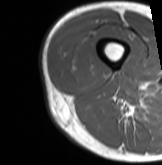
MRI of an extremity soft-tissue mass, one axial slice; position 13 of 61 along the scan axis; MR volume resampled by the dataset authors to the PET/CT grid (not the native acquisition matrix); 3.27 mm slice thickness; 162 × 165 image matrix. Male patient. Case-level facts recorded for this patient, not image findings: histological type: poorly differentiated synovial sarcoma; grade: high; site of the primary tumour: right buttock.
Structures marked on this image (expert contour drawn on MRI and transferred to this co-registered scan by the dataset authors):
- gross tumour volume including surrounding oedema: bounding box (x1, y1, x2, y2) in pixels: (64, 47, 94, 80)